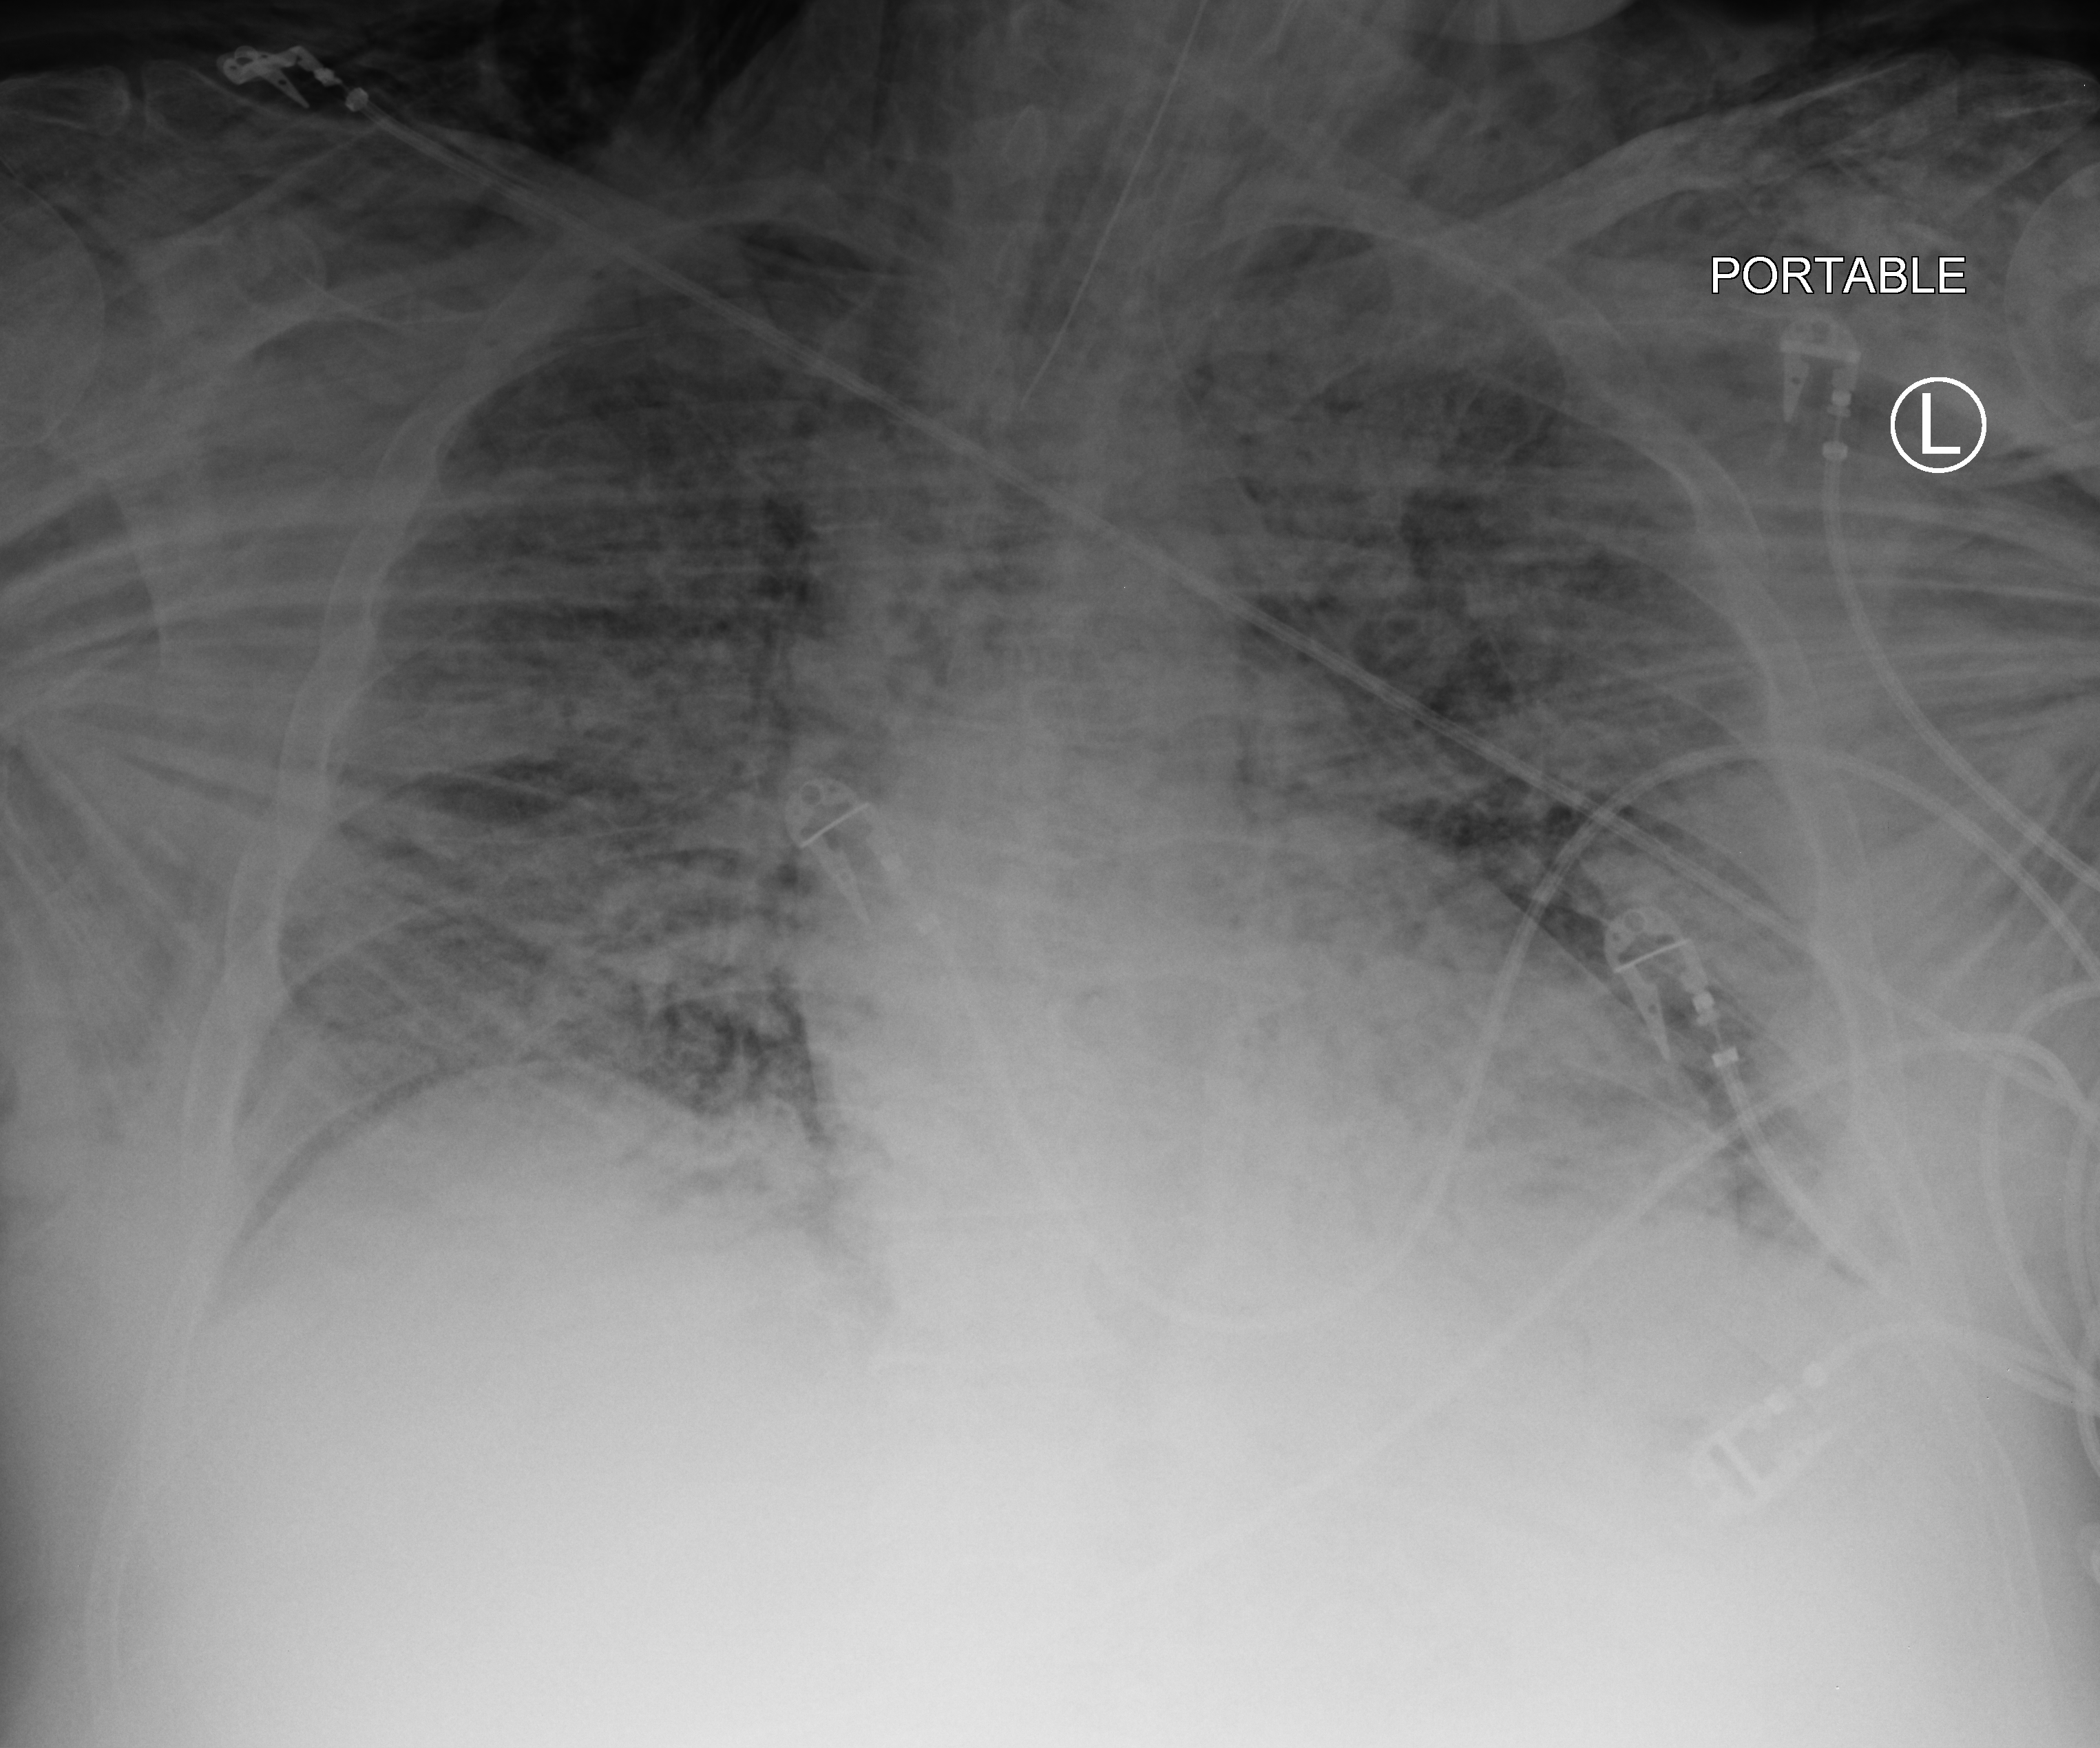
Bedside chest radiograph (computed radiography), anteroposterior (AP) projection. Patient hospitalised with COVID-19, aged 18–59 years.
Admission-level facts for this patient (not findings on this image; timing relative to this image not recorded): admitted to intensive care during this hospital stay: yes.